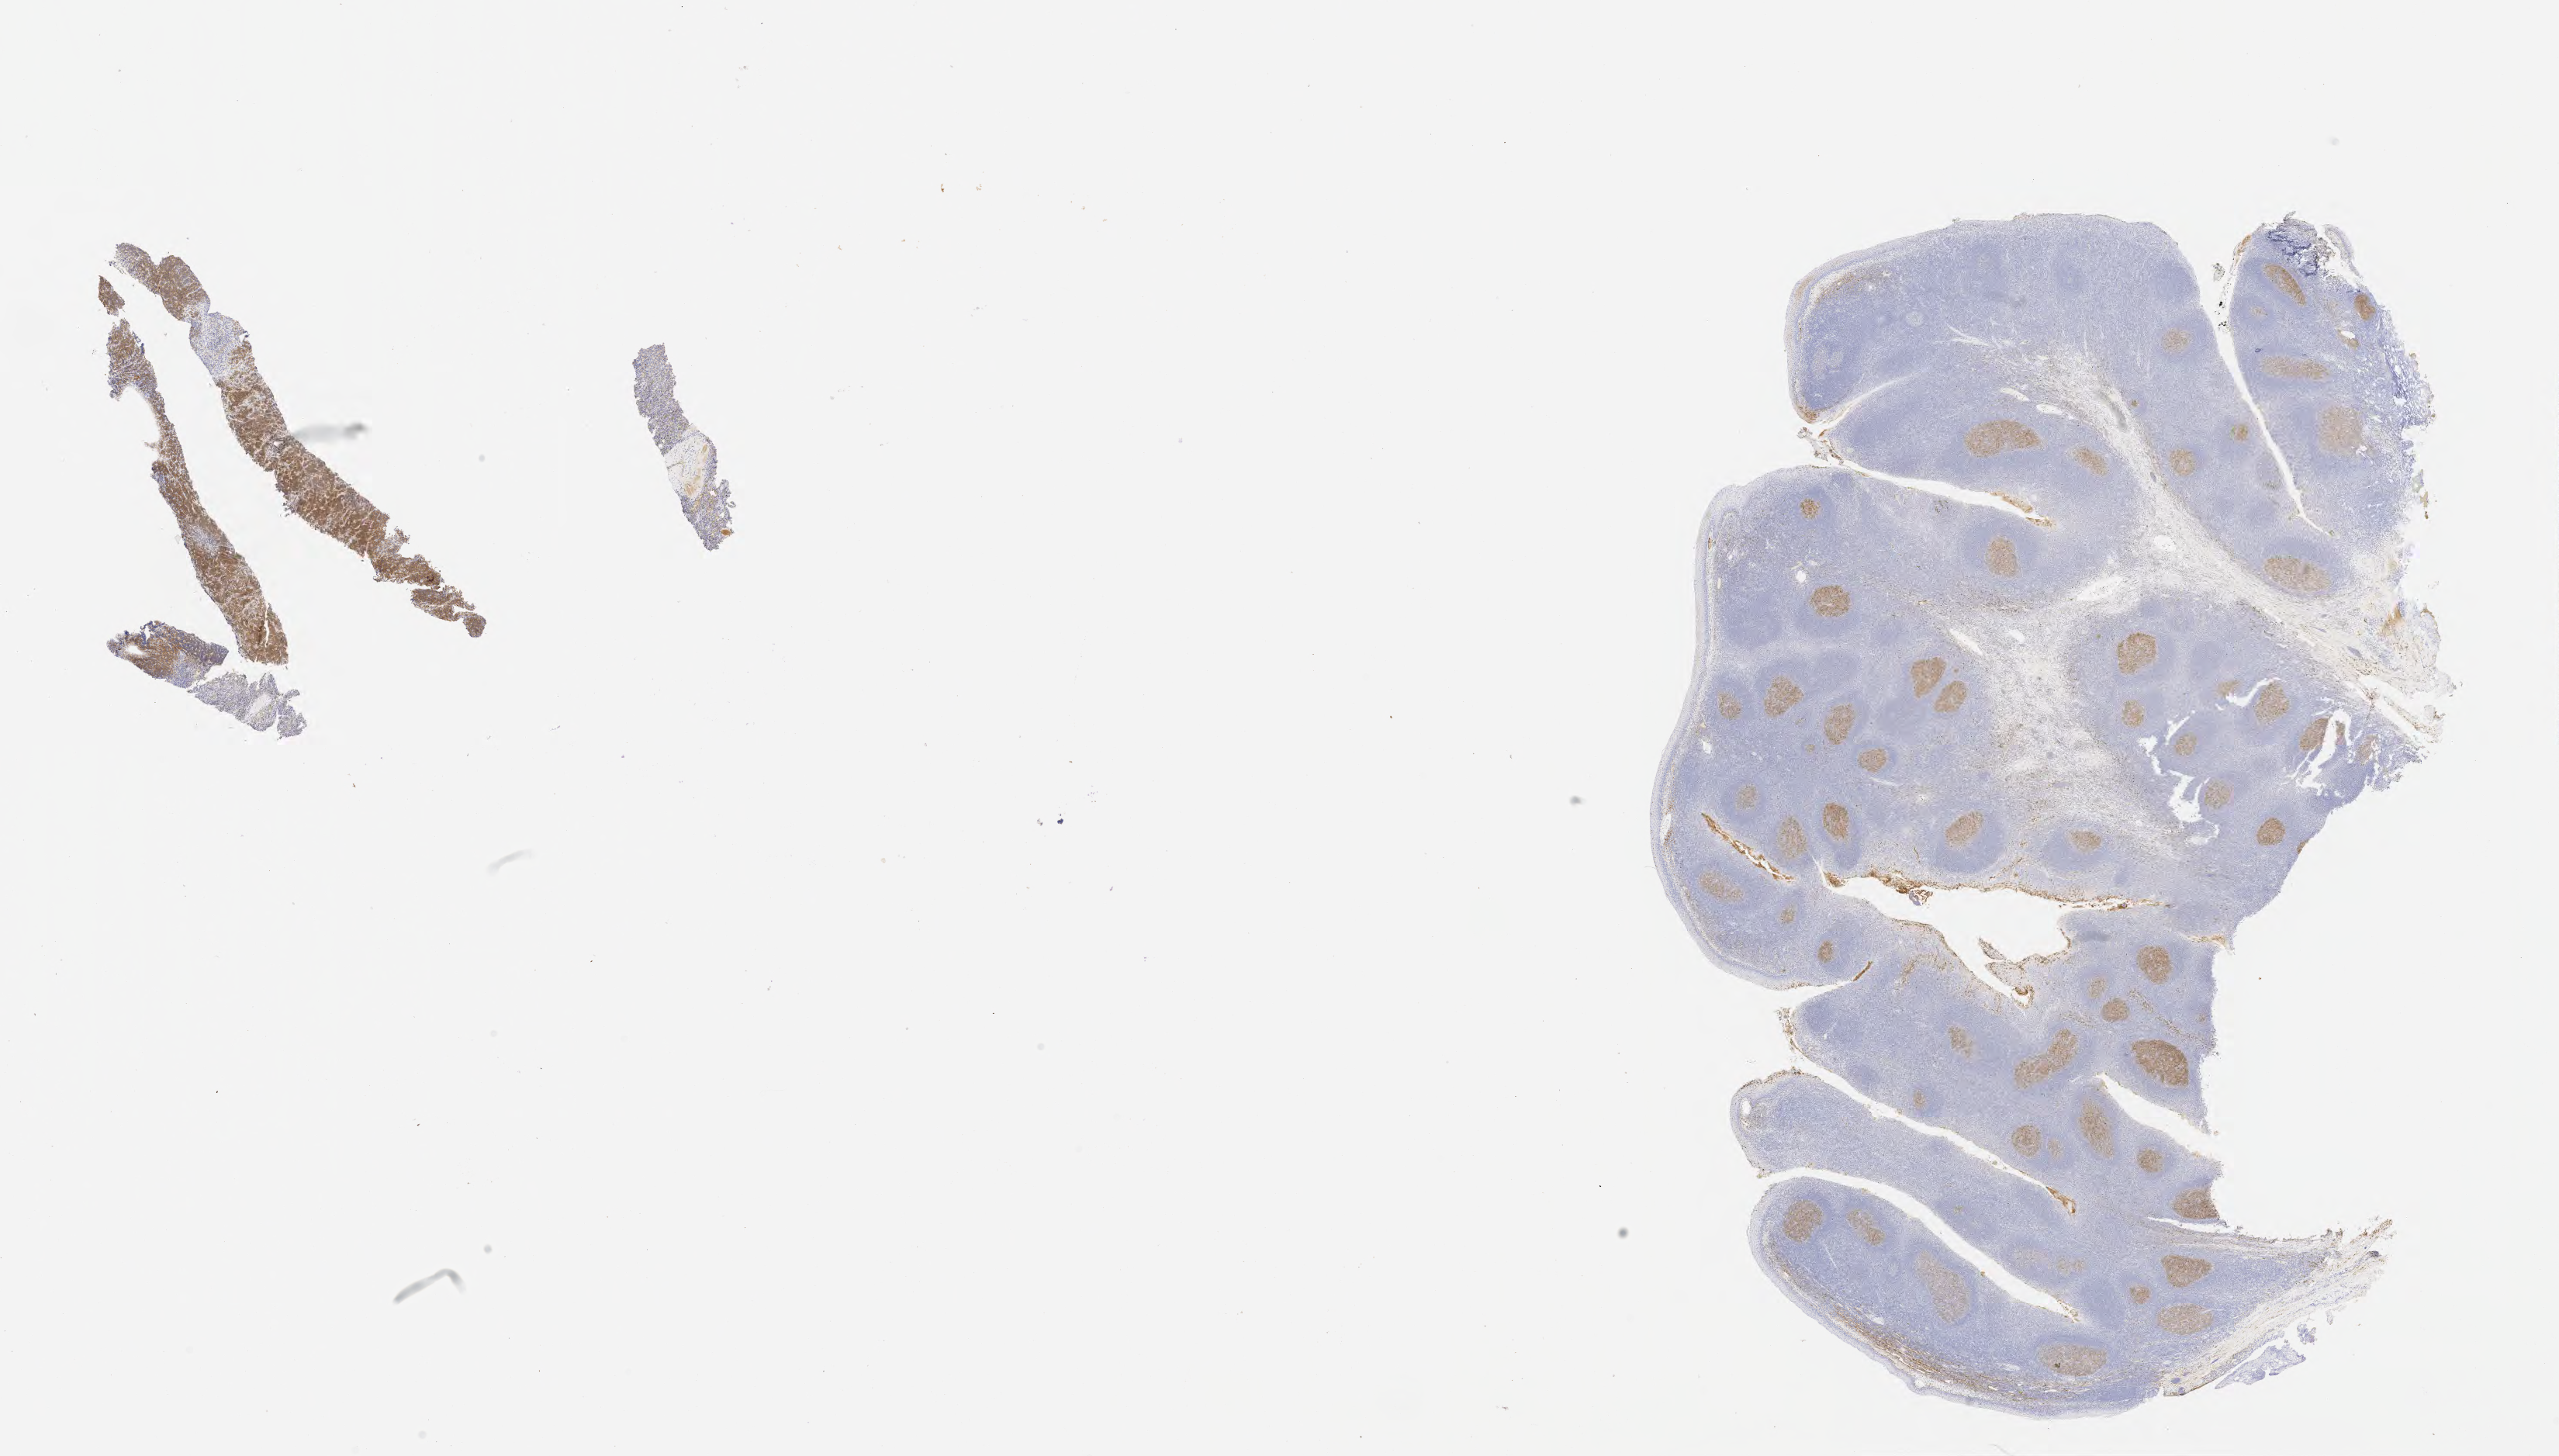
IHC for CD10, whole-slide image — low-resolution overview of the scanned area, about 26.7 x 15.2 mm. Tumor tissue. Patient: male, age 13 years.
Histologic diagnosis: Diffuse large B-cell lymphoma, NOS.